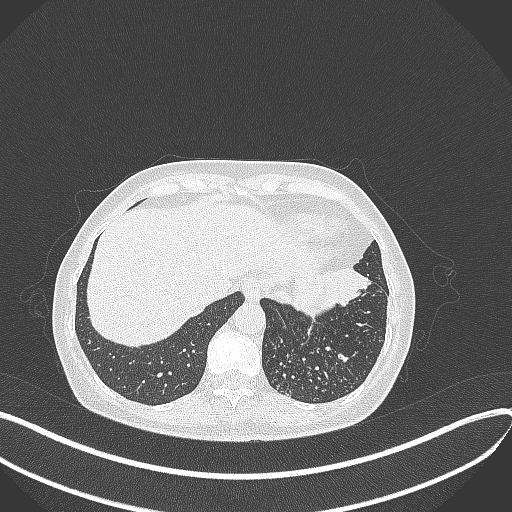
Chest CT, one axial slice. Position 84 of 429 along the scan axis. Reconstruction kernel B70f. 100 kVp. Lung window (W 1500 / L -600 HU). 1 mm slice thickness. 512 × 512 image matrix. Patient: female, 63 years. Case-level facts recorded for this patient, not image findings: clinical TNM (as recorded): T1b N0 M0.
Annotated regions visible in this slice (rectangle marked by the reading radiologist):
- lung tumour (recorded histology: adenocarcinoma): bounding box <304,264,371,315> (left, top, right, bottom; pixels)